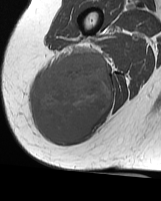
MRI of an extremity soft-tissue mass, one axial slice. Position 24 of 70 along the scan axis. MR volume resampled by the dataset authors to the PET/CT grid (not the native acquisition matrix). 161 × 201 image matrix. Female patient. Case-level facts recorded for this patient, not image findings: histological type: synovial sarcoma; grade: intermediate; site of the primary tumour: right buttock.
Structures marked on this image (expert contour drawn on MRI and transferred to this co-registered scan by the dataset authors):
- gross tumour volume including surrounding oedema: bounding box <31,47,112,144> (left, top, right, bottom; pixels)
- gross tumour volume (mass): <31,51,112,144>